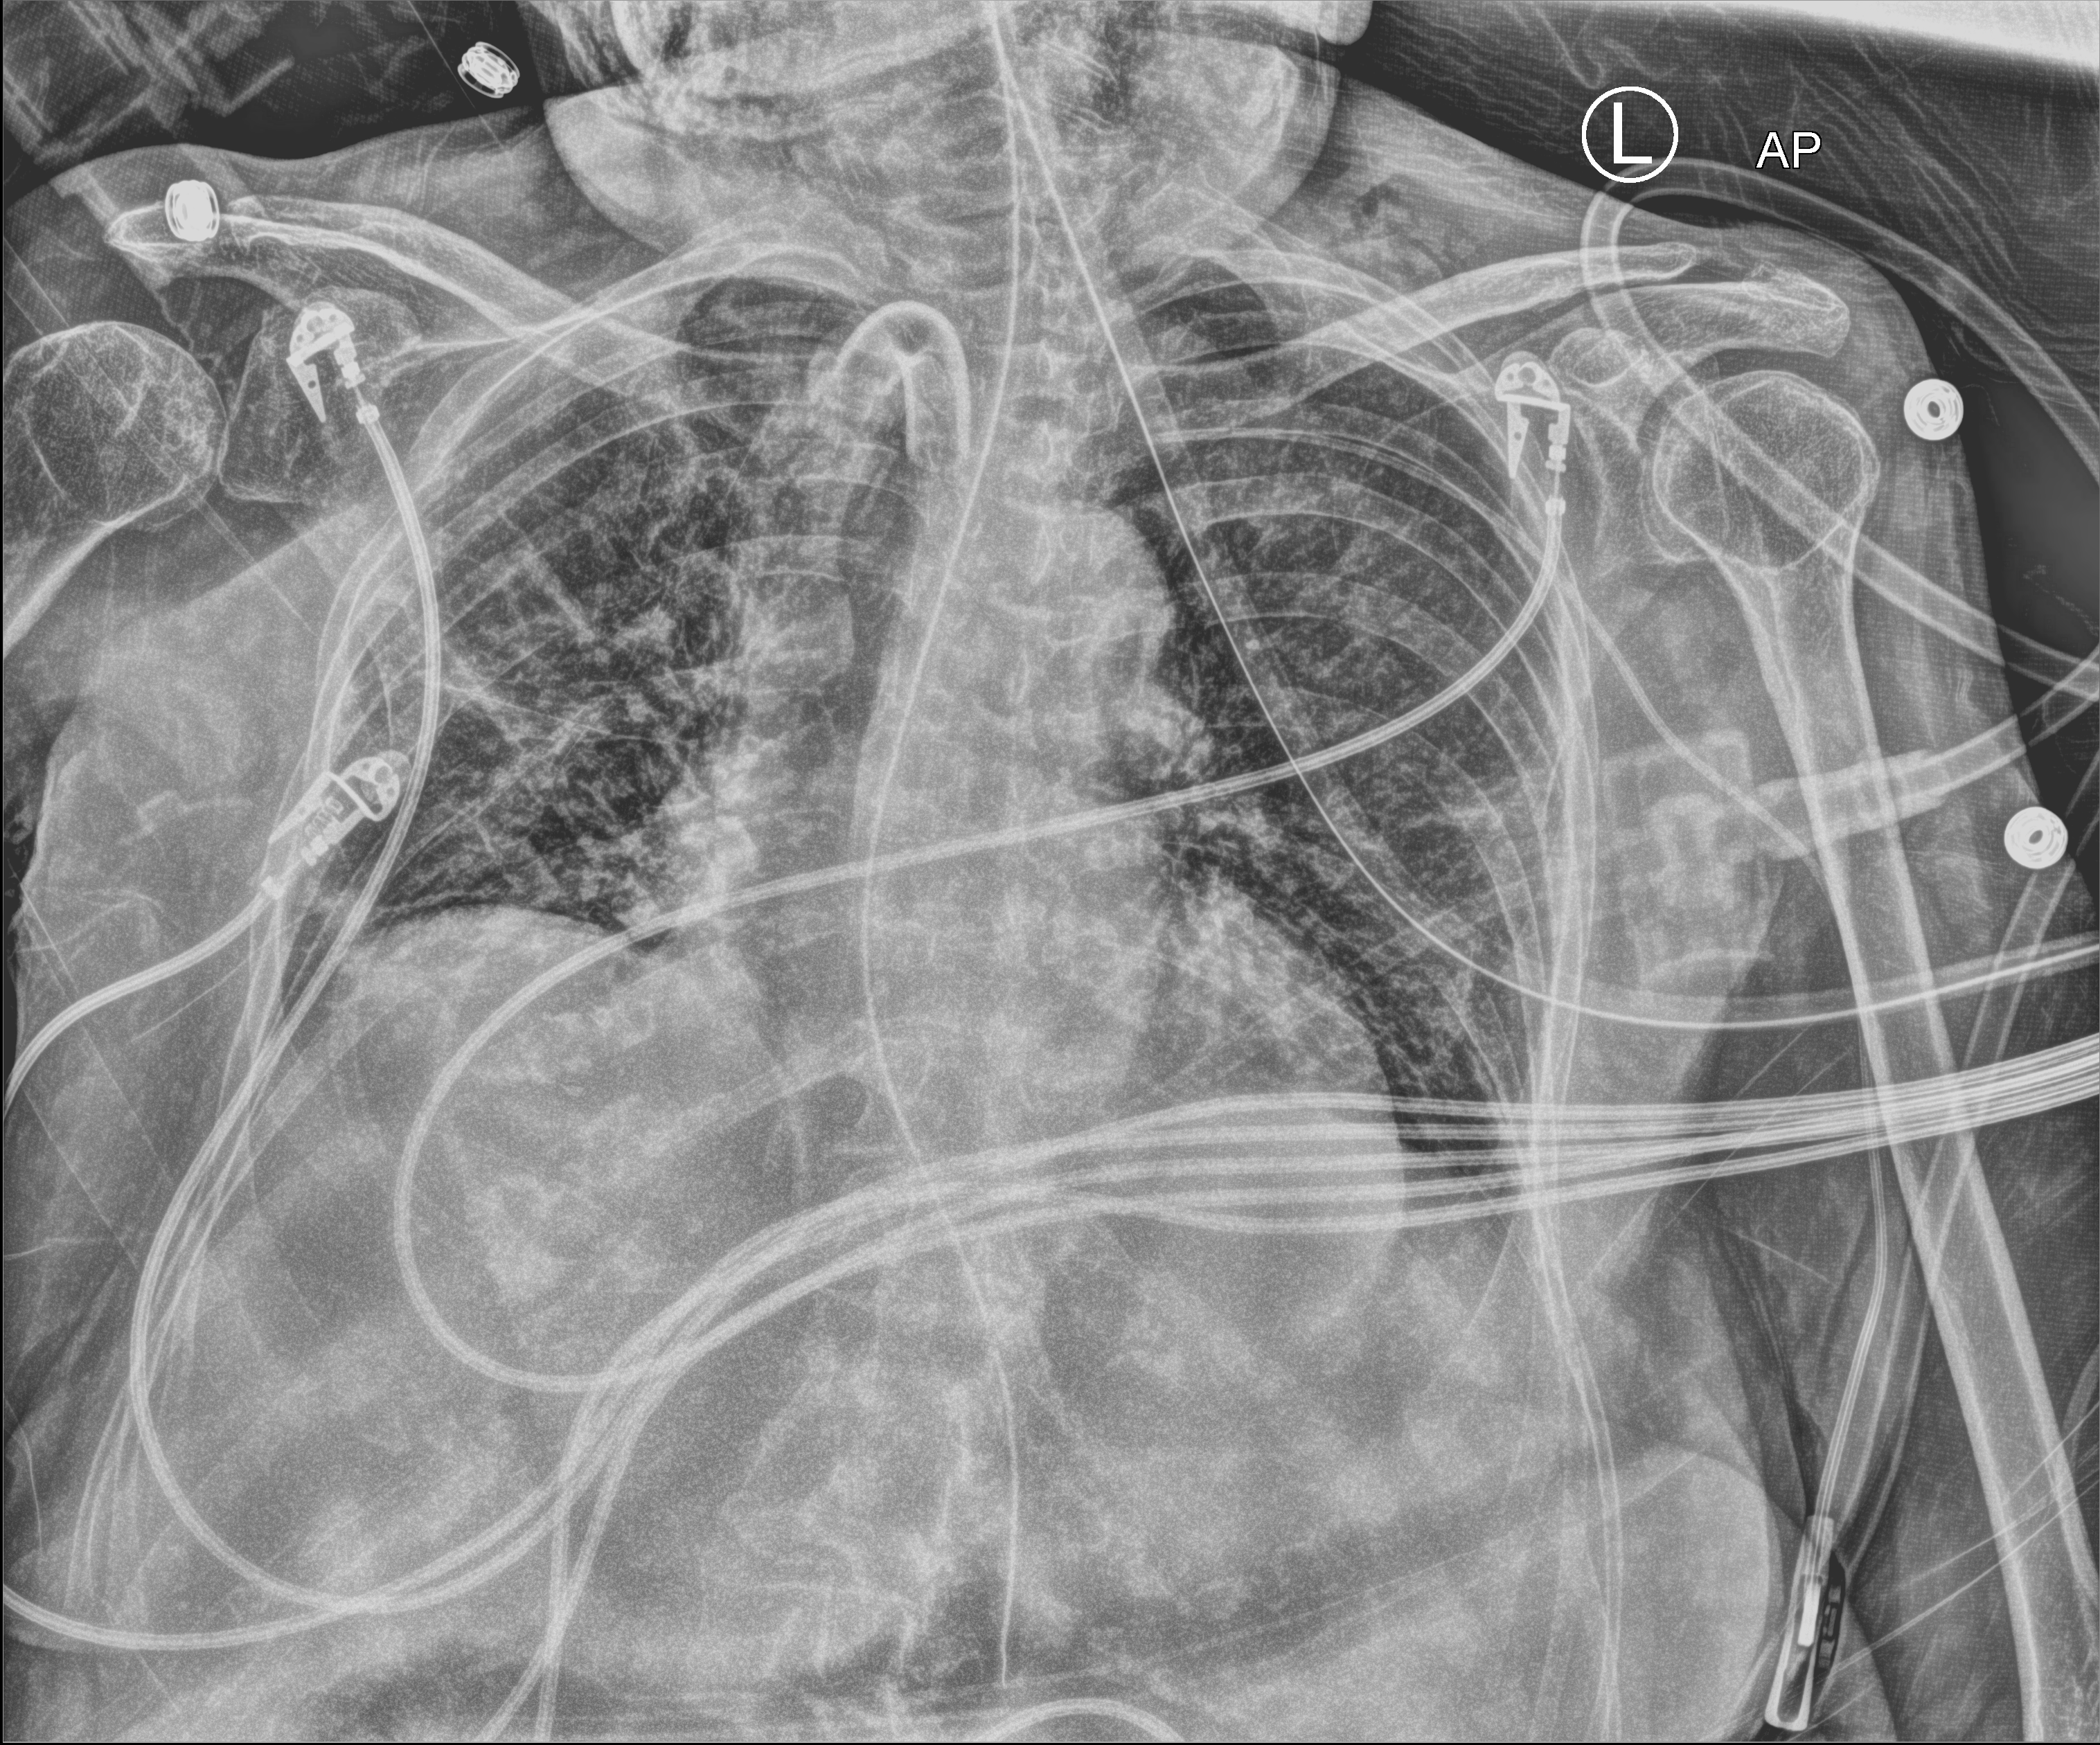
Chest X-ray (portable); anteroposterior (AP) projection. Female patient hospitalised with COVID-19, age 75–90 years.
From the hospital-stay record, not from the radiograph (when in the stay this image was taken is not recorded): diabetes (admission record): no; admitted to intensive care during this hospital stay: yes.